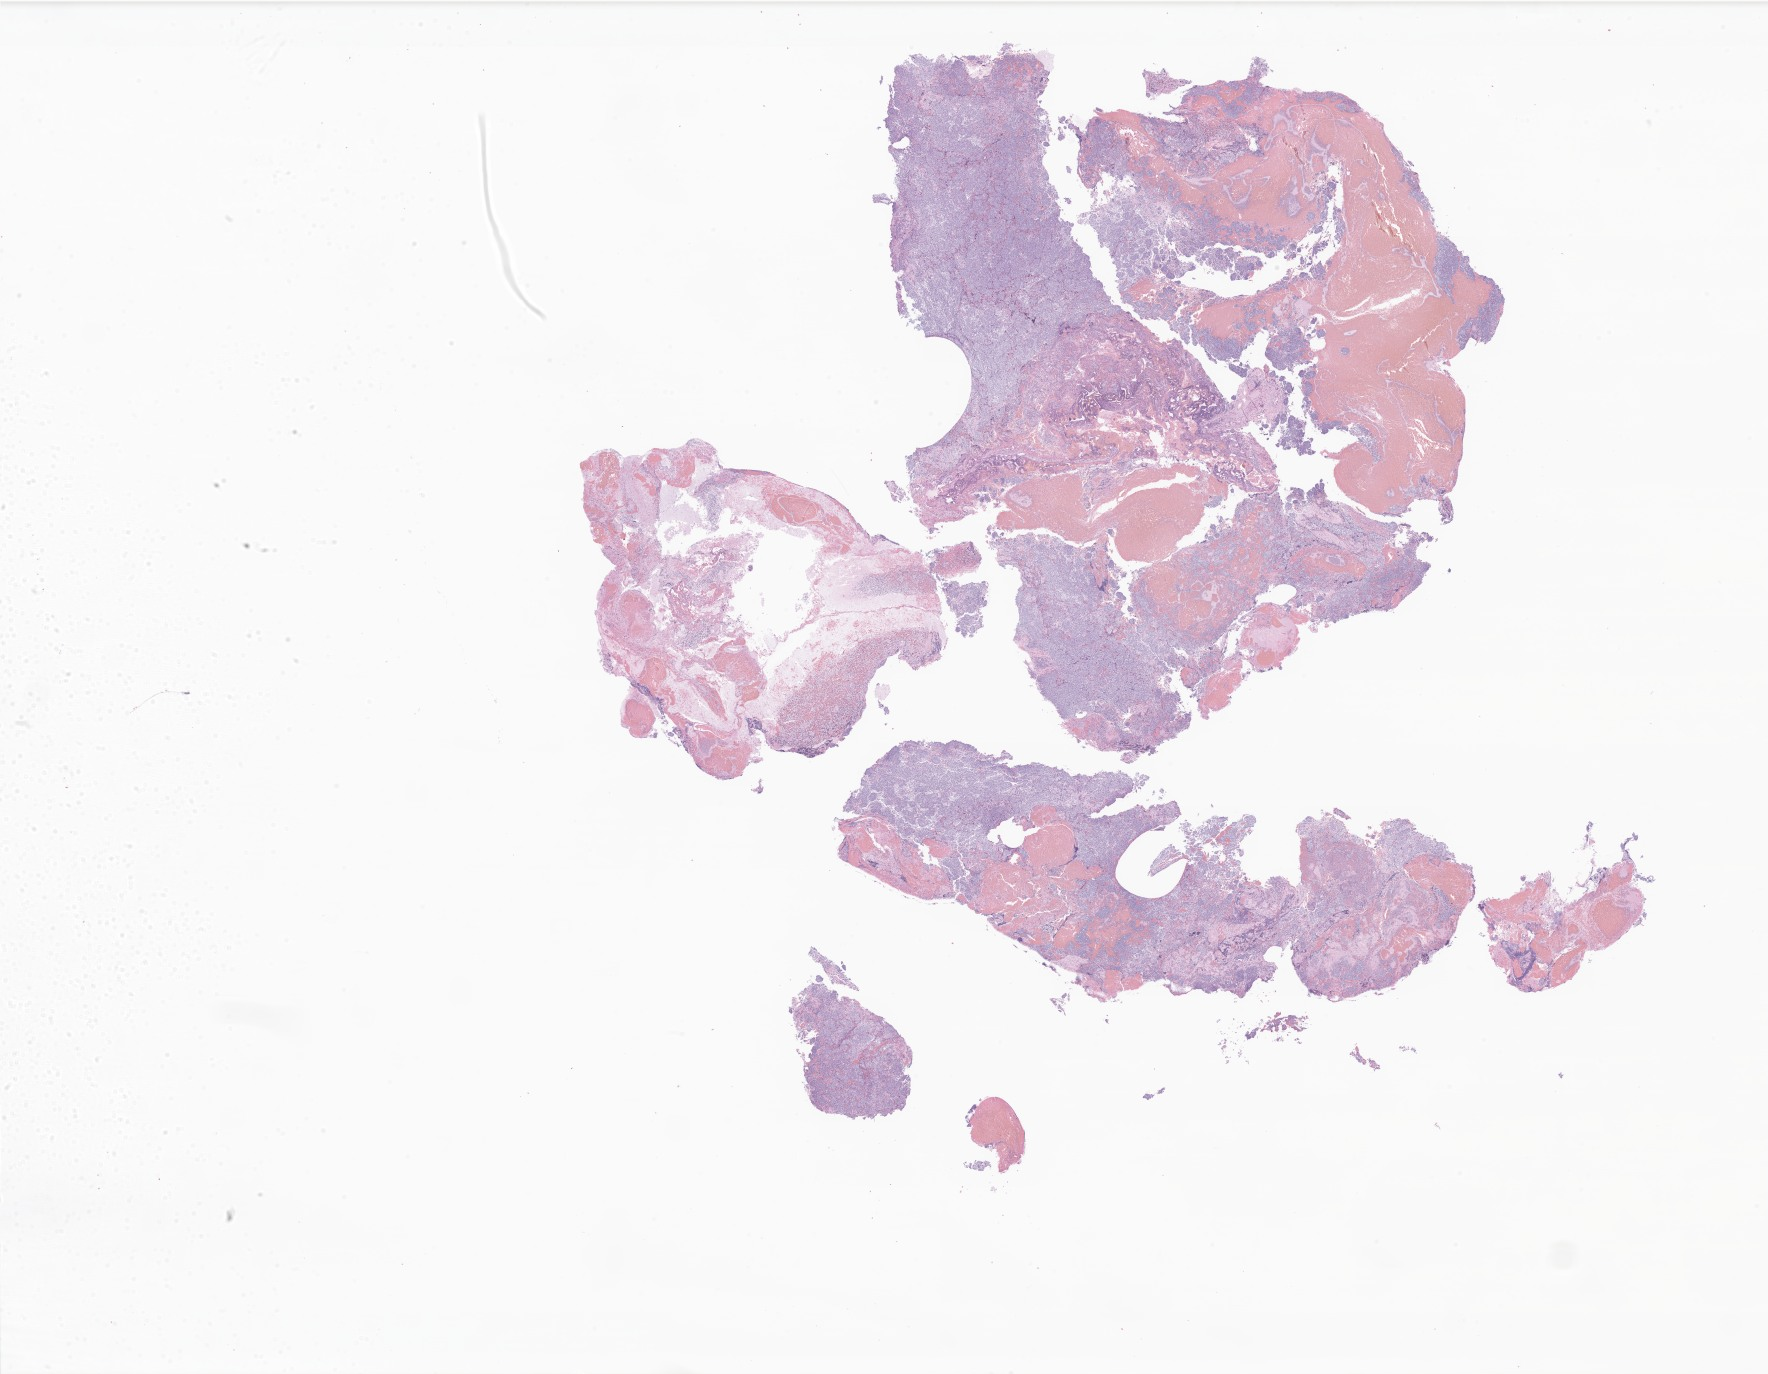
Whole-slide image, H&E stain of tumor tissue from the brain, shown as a low-resolution overview of the whole scanned area (about 29.8 x 23.2 mm); formalin-fixed paraffin-embedded section. Patient: female, age 84 months.
Recorded diagnosis: Medulloblastoma, NOS.